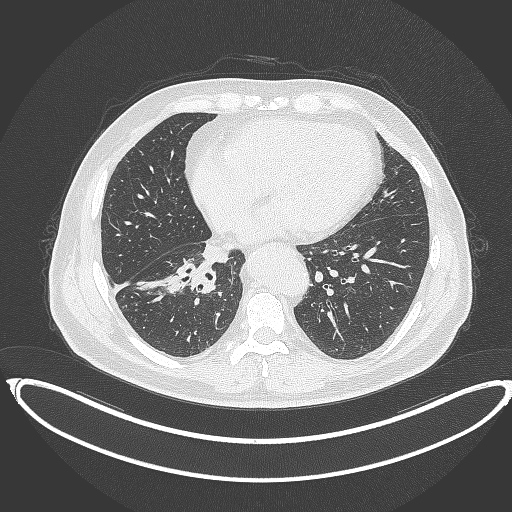
Chest CT, one axial slice. Slice 154 of 387 in the series (ordered by position). Reconstruction kernel B70f. 120 kVp. Lung window (W 1500 / L -600 HU). 512 × 512 image matrix, field of view 448 × 448 mm. Patient: male, 61 years. From the clinical record (not read from this slice): clinical TNM (as recorded): T1b N1 M0.
Structures marked on this image (bounding box drawn by a radiologist):
- lung tumour (recorded histology: squamous cell carcinoma): bounding box (x1, y1, x2, y2) in pixels: (164, 260, 218, 298)